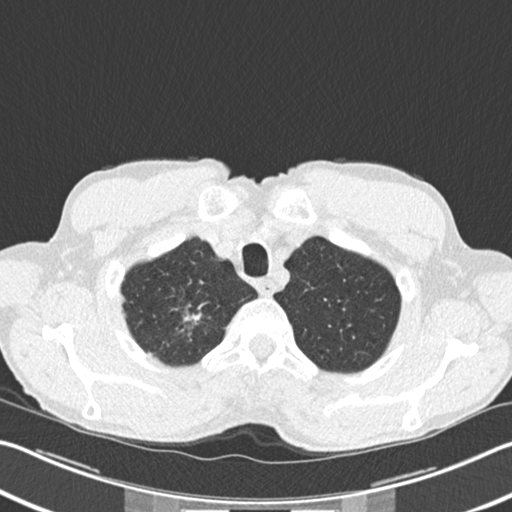
Axial slice from a low-dose chest CT screening exam. Second screening round (one year after baseline). Lung window (W 1500 / L -600 HU). 2 mm slice thickness. Male participant, aged 62 years at enrolment. Former smoker at enrolment.
Lesion marked by an expert reader, box from (x=166, y=299) to (x=209, y=344) px. The screening reader recorded 2 non-calcified nodules or masses ≥4 mm on this exam (right upper lobe, right upper lobe); which of them this box marks is not recorded. Official screen result: positive, change unspecified: nodule(s) >= 4 mm or enlarging nodule(s), mass(es), or other non-specific abnormalities suspicious for lung cancer. Participant outcome: lung cancer diagnosed 5 days after this screen — bronchiolo-alveolar adenocarcinoma, NOS, right upper lobe, well differentiated (G1), stage IA (AJCC 6th edition), 15 mm at pathology.